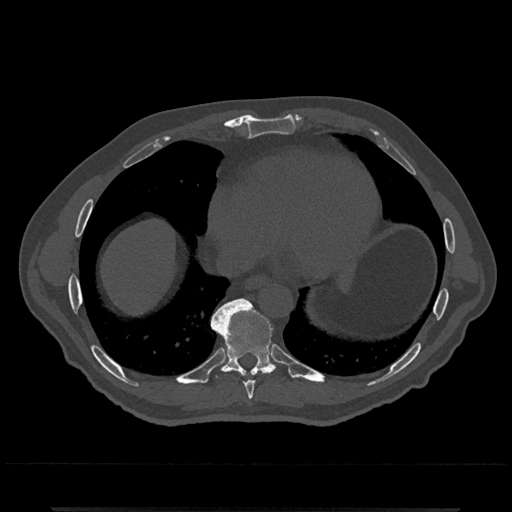
CT including the spine, one axial slice. Position 633 of 797 along the scan axis. 120 kVp. Bone window (W 1800 / L 400 HU). 0.5 mm slice thickness. 512 × 512 image matrix, field of view 393 × 393 mm. Male patient, age 67 years. Case-level facts recorded for this patient, not image findings: primary cancer: prostate.
Annotated regions visible in this slice (semi-automatic segmentation, software-assisted and operator-edited):
- T8 vertebra: bounding box [x1, y1, x2, y2] px = [245, 380, 255, 400]
- T9 vertebra: [211, 299, 278, 379]